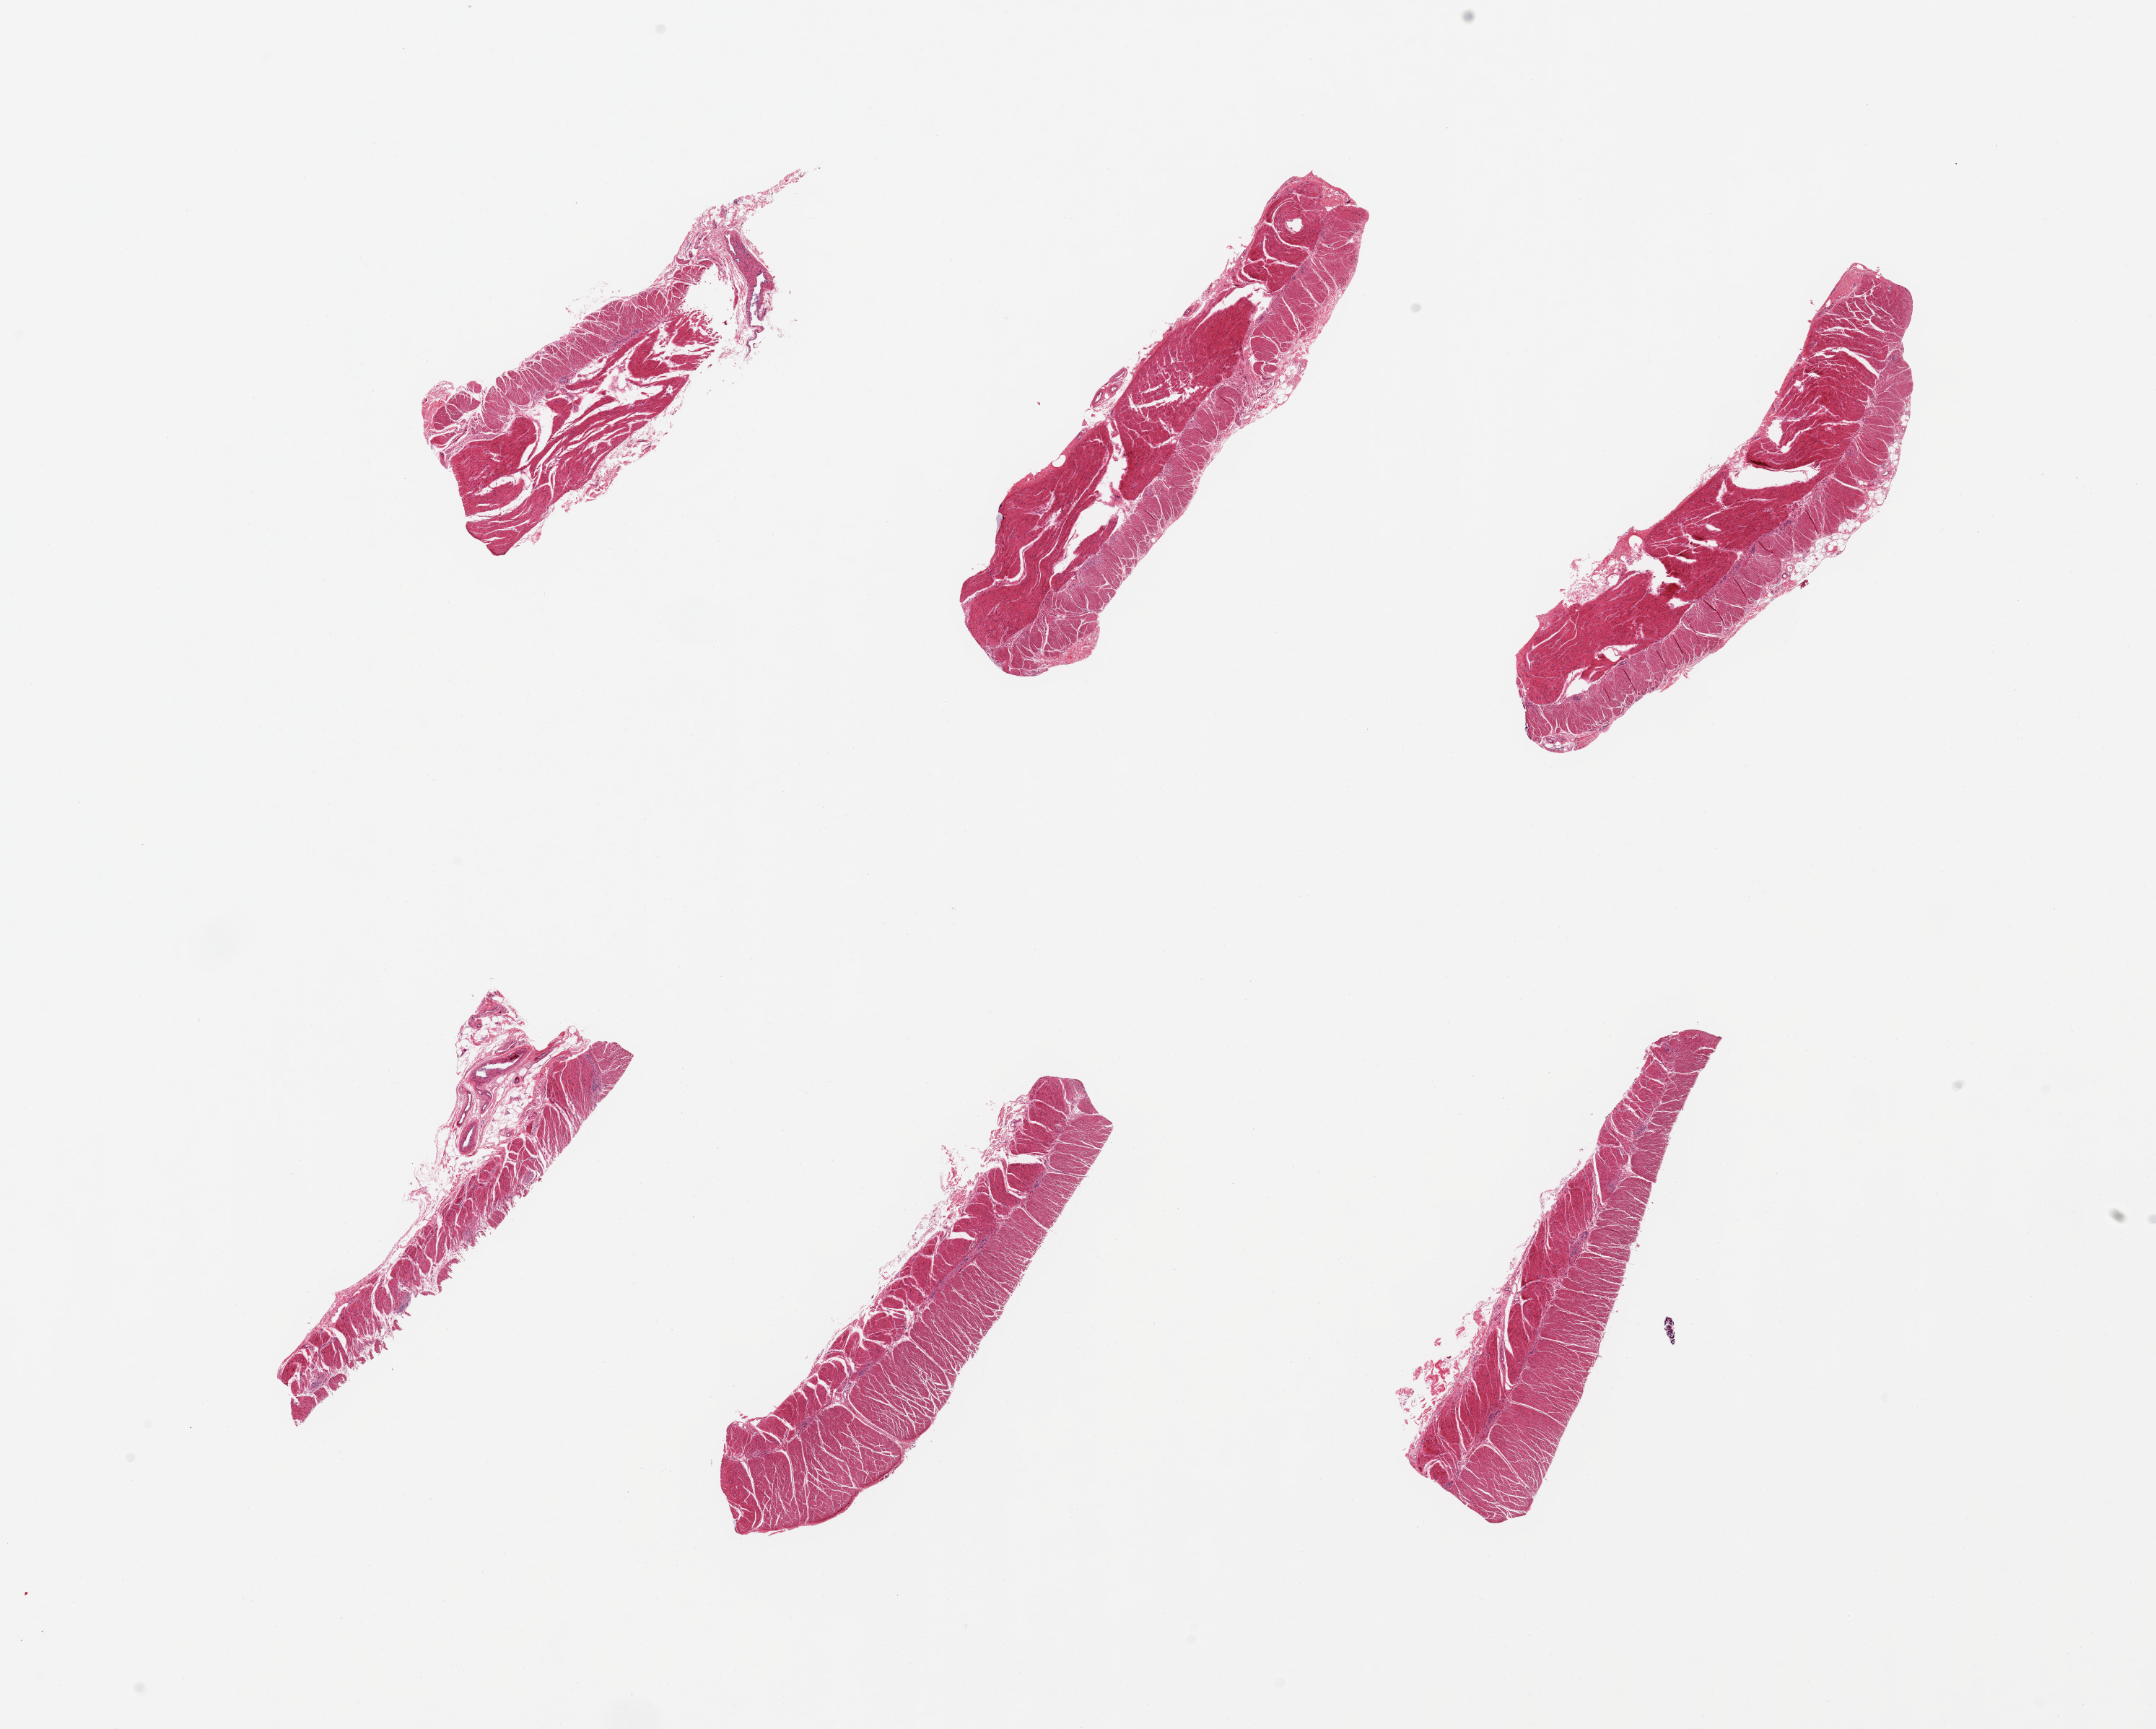
Digitized hematoxylin and eosin (H&E)-stained section, brightfield, a low-resolution overview of the entire scanned area, about 23.6 x 18.9 mm. PAXgene-fixed paraffin-embedded (PFPE) section. Target tissue: sigmoid colon. Tissue donor sample. Donor: male.
* review note (as recorded): 6 pieces, all muscularis